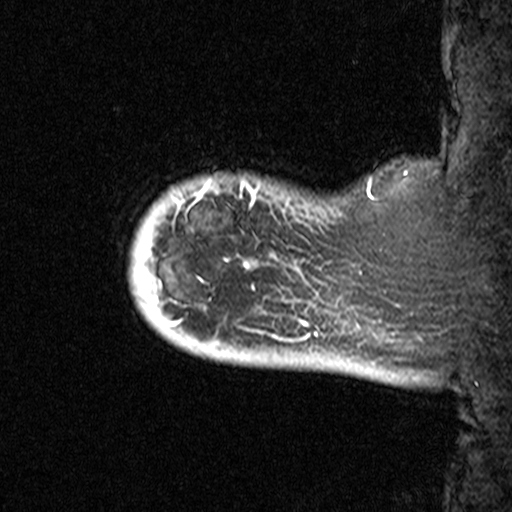
Breast MRI (dynamic contrast-enhanced), one sagittal slice. Position 4 of 44 along the scan axis. Dynamic contrast-enhanced study with each time point stored as its own series, time point 2 of 3 at this slice position (early post-contrast, ordered by acquisition time). 1.5 T. TE 4.5 ms, TR 11 ms. 3.27 mm slice thickness. 512 × 512 image matrix. Female patient, age 53 years. From the clinical record (not read from this slice): setting: breast cancer imaged before/during neoadjuvant chemotherapy; receptor status: HR-positive, HER2-negative.
Outlined on this slice (semi-automatically segmented with operator editing):
- analysis volume of interest (the breast-tissue region the enhancement analysis was run in; not a lesion): bounding box (x1, y1, x2, y2) in pixels: (116, 158, 311, 367)
- tumour enhancement mask (voxels above the 90 % enhancement threshold inside the analysis volume of interest): (186, 184, 243, 220)